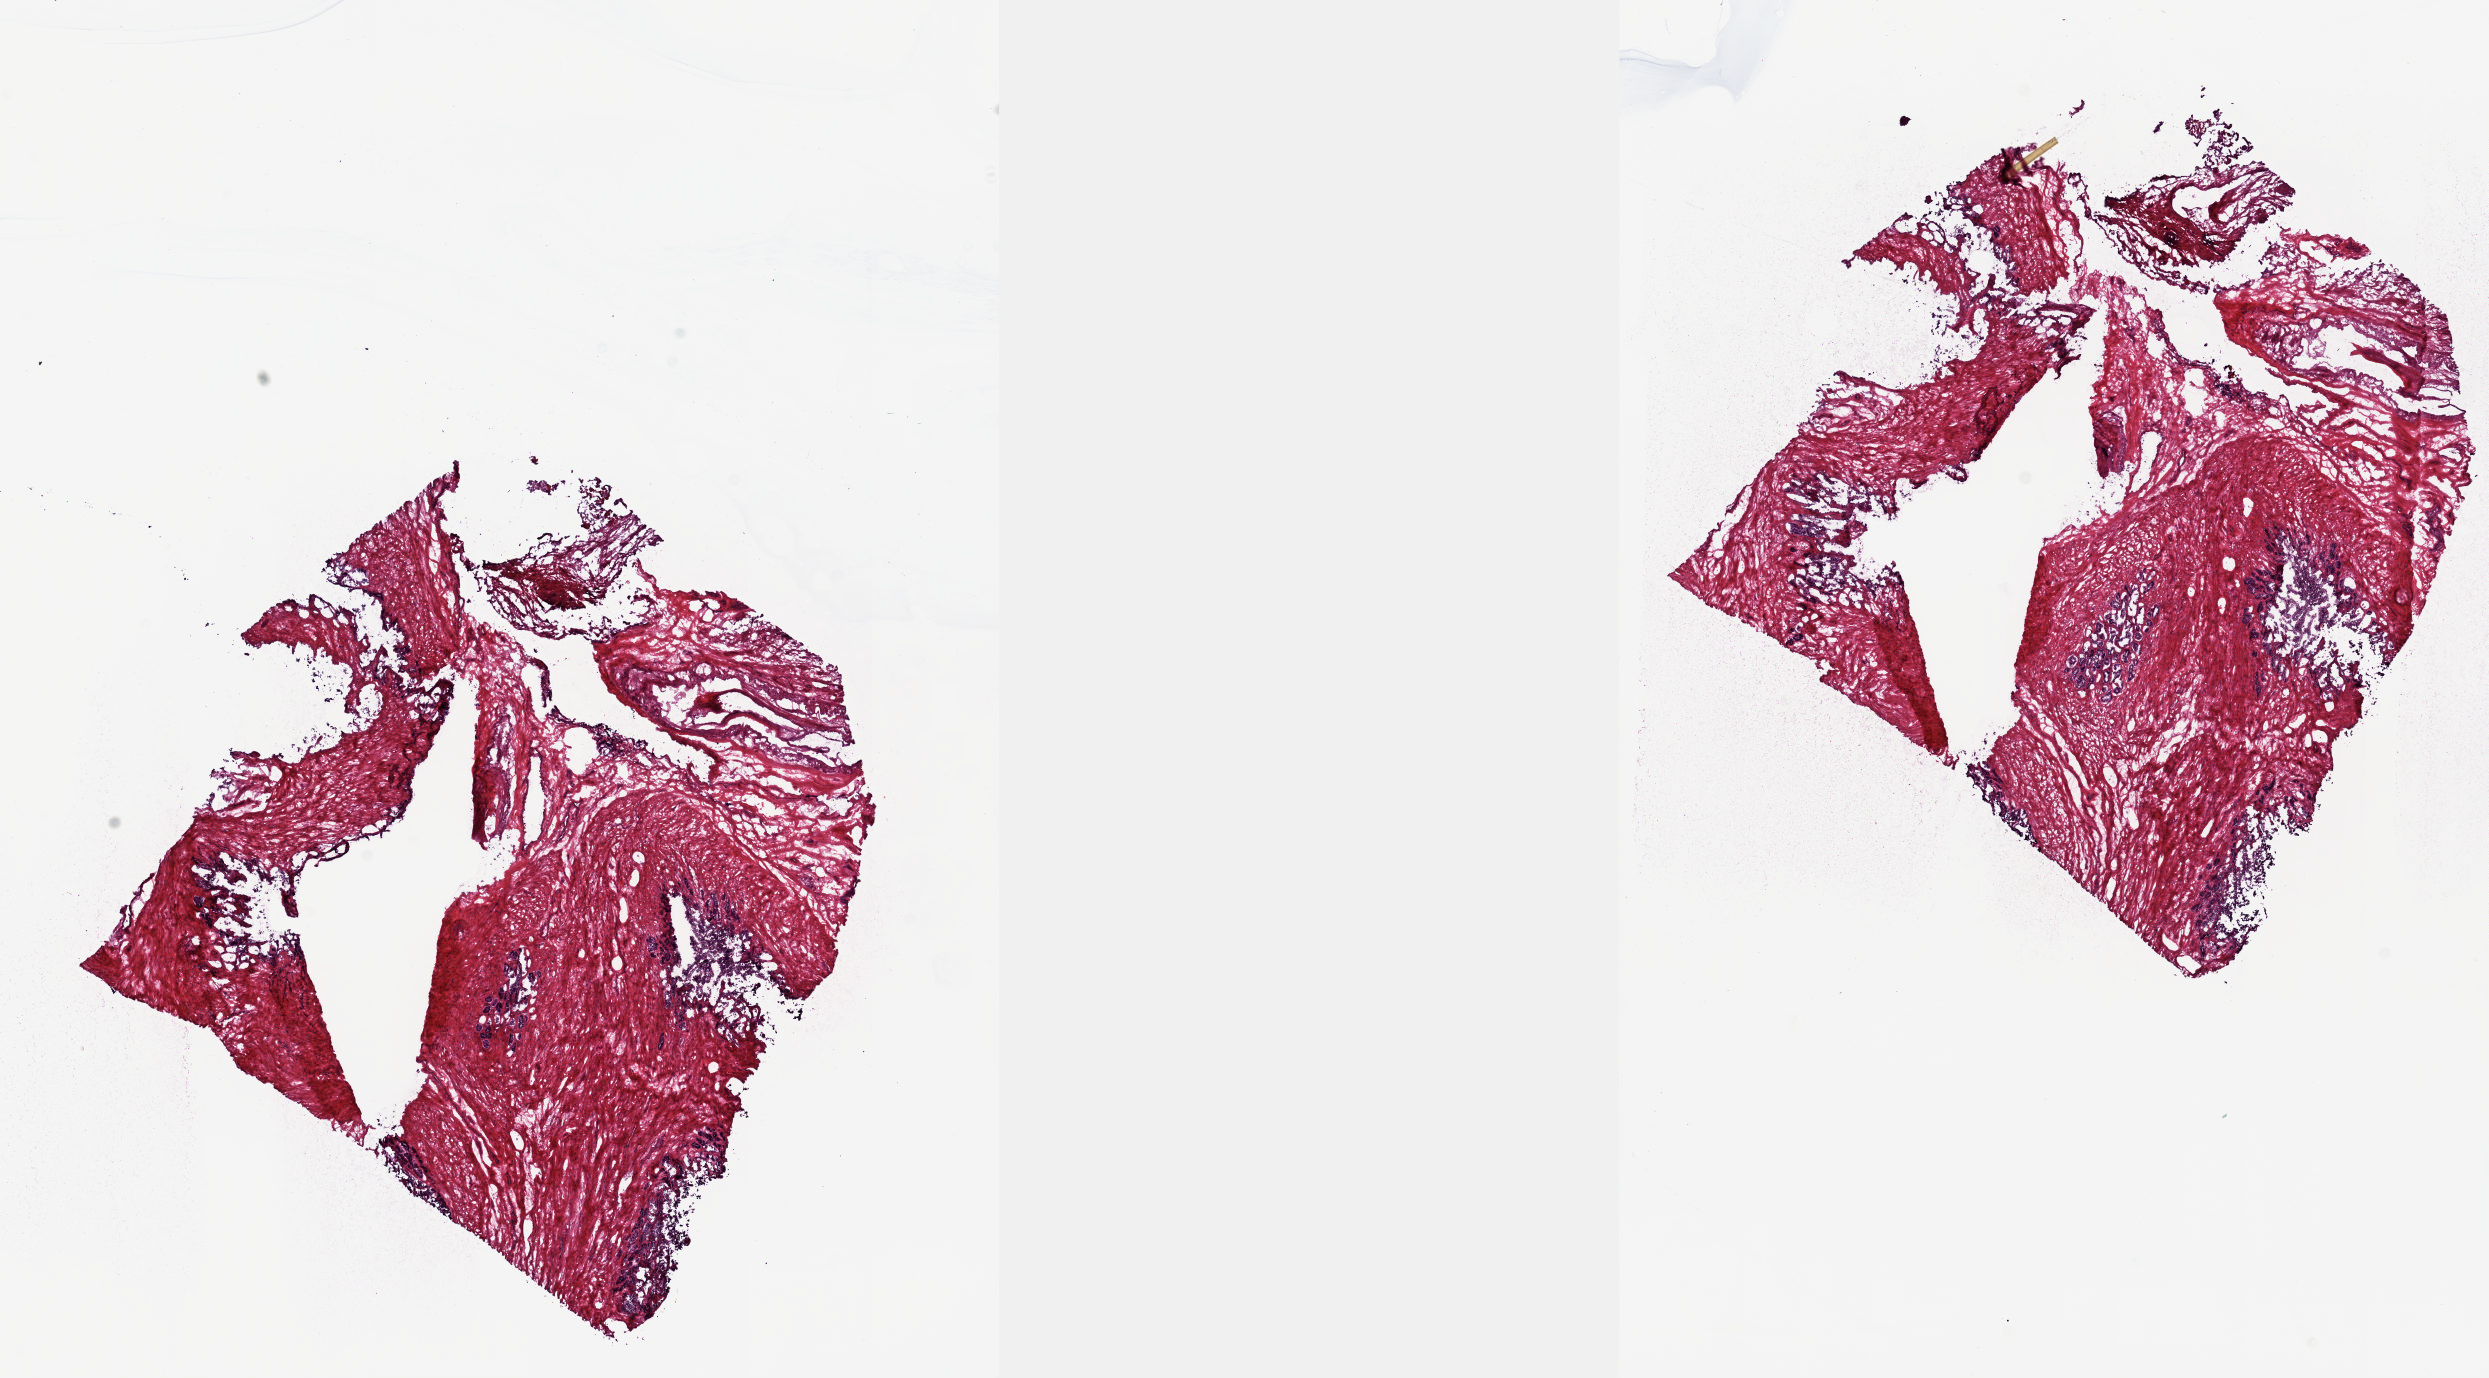
H&E-stained whole-slide image, a low-resolution overview of the entire scanned area, about 20.1 x 11.1 mm (from a 20x scan), frozen section from the top of the tissue portion, solid tissue normal (non-tumour tissue) sample from the prostate. Male patient; age at initial diagnosis 61 years. Slide review estimates, as recorded: tumour cells 0%, tumour nuclei 0%, normal cells 30%, stromal cells 70%, necrosis 0%. Infiltration values recorded for this section: lymphocyte infiltration 40%, monocyte infiltration 20%, neutrophil infiltration 20%.
This section: solid tissue normal (non-tumour) sample from the same patient. Patient diagnosis: Adenocarcinoma, NOS (prostate gland).